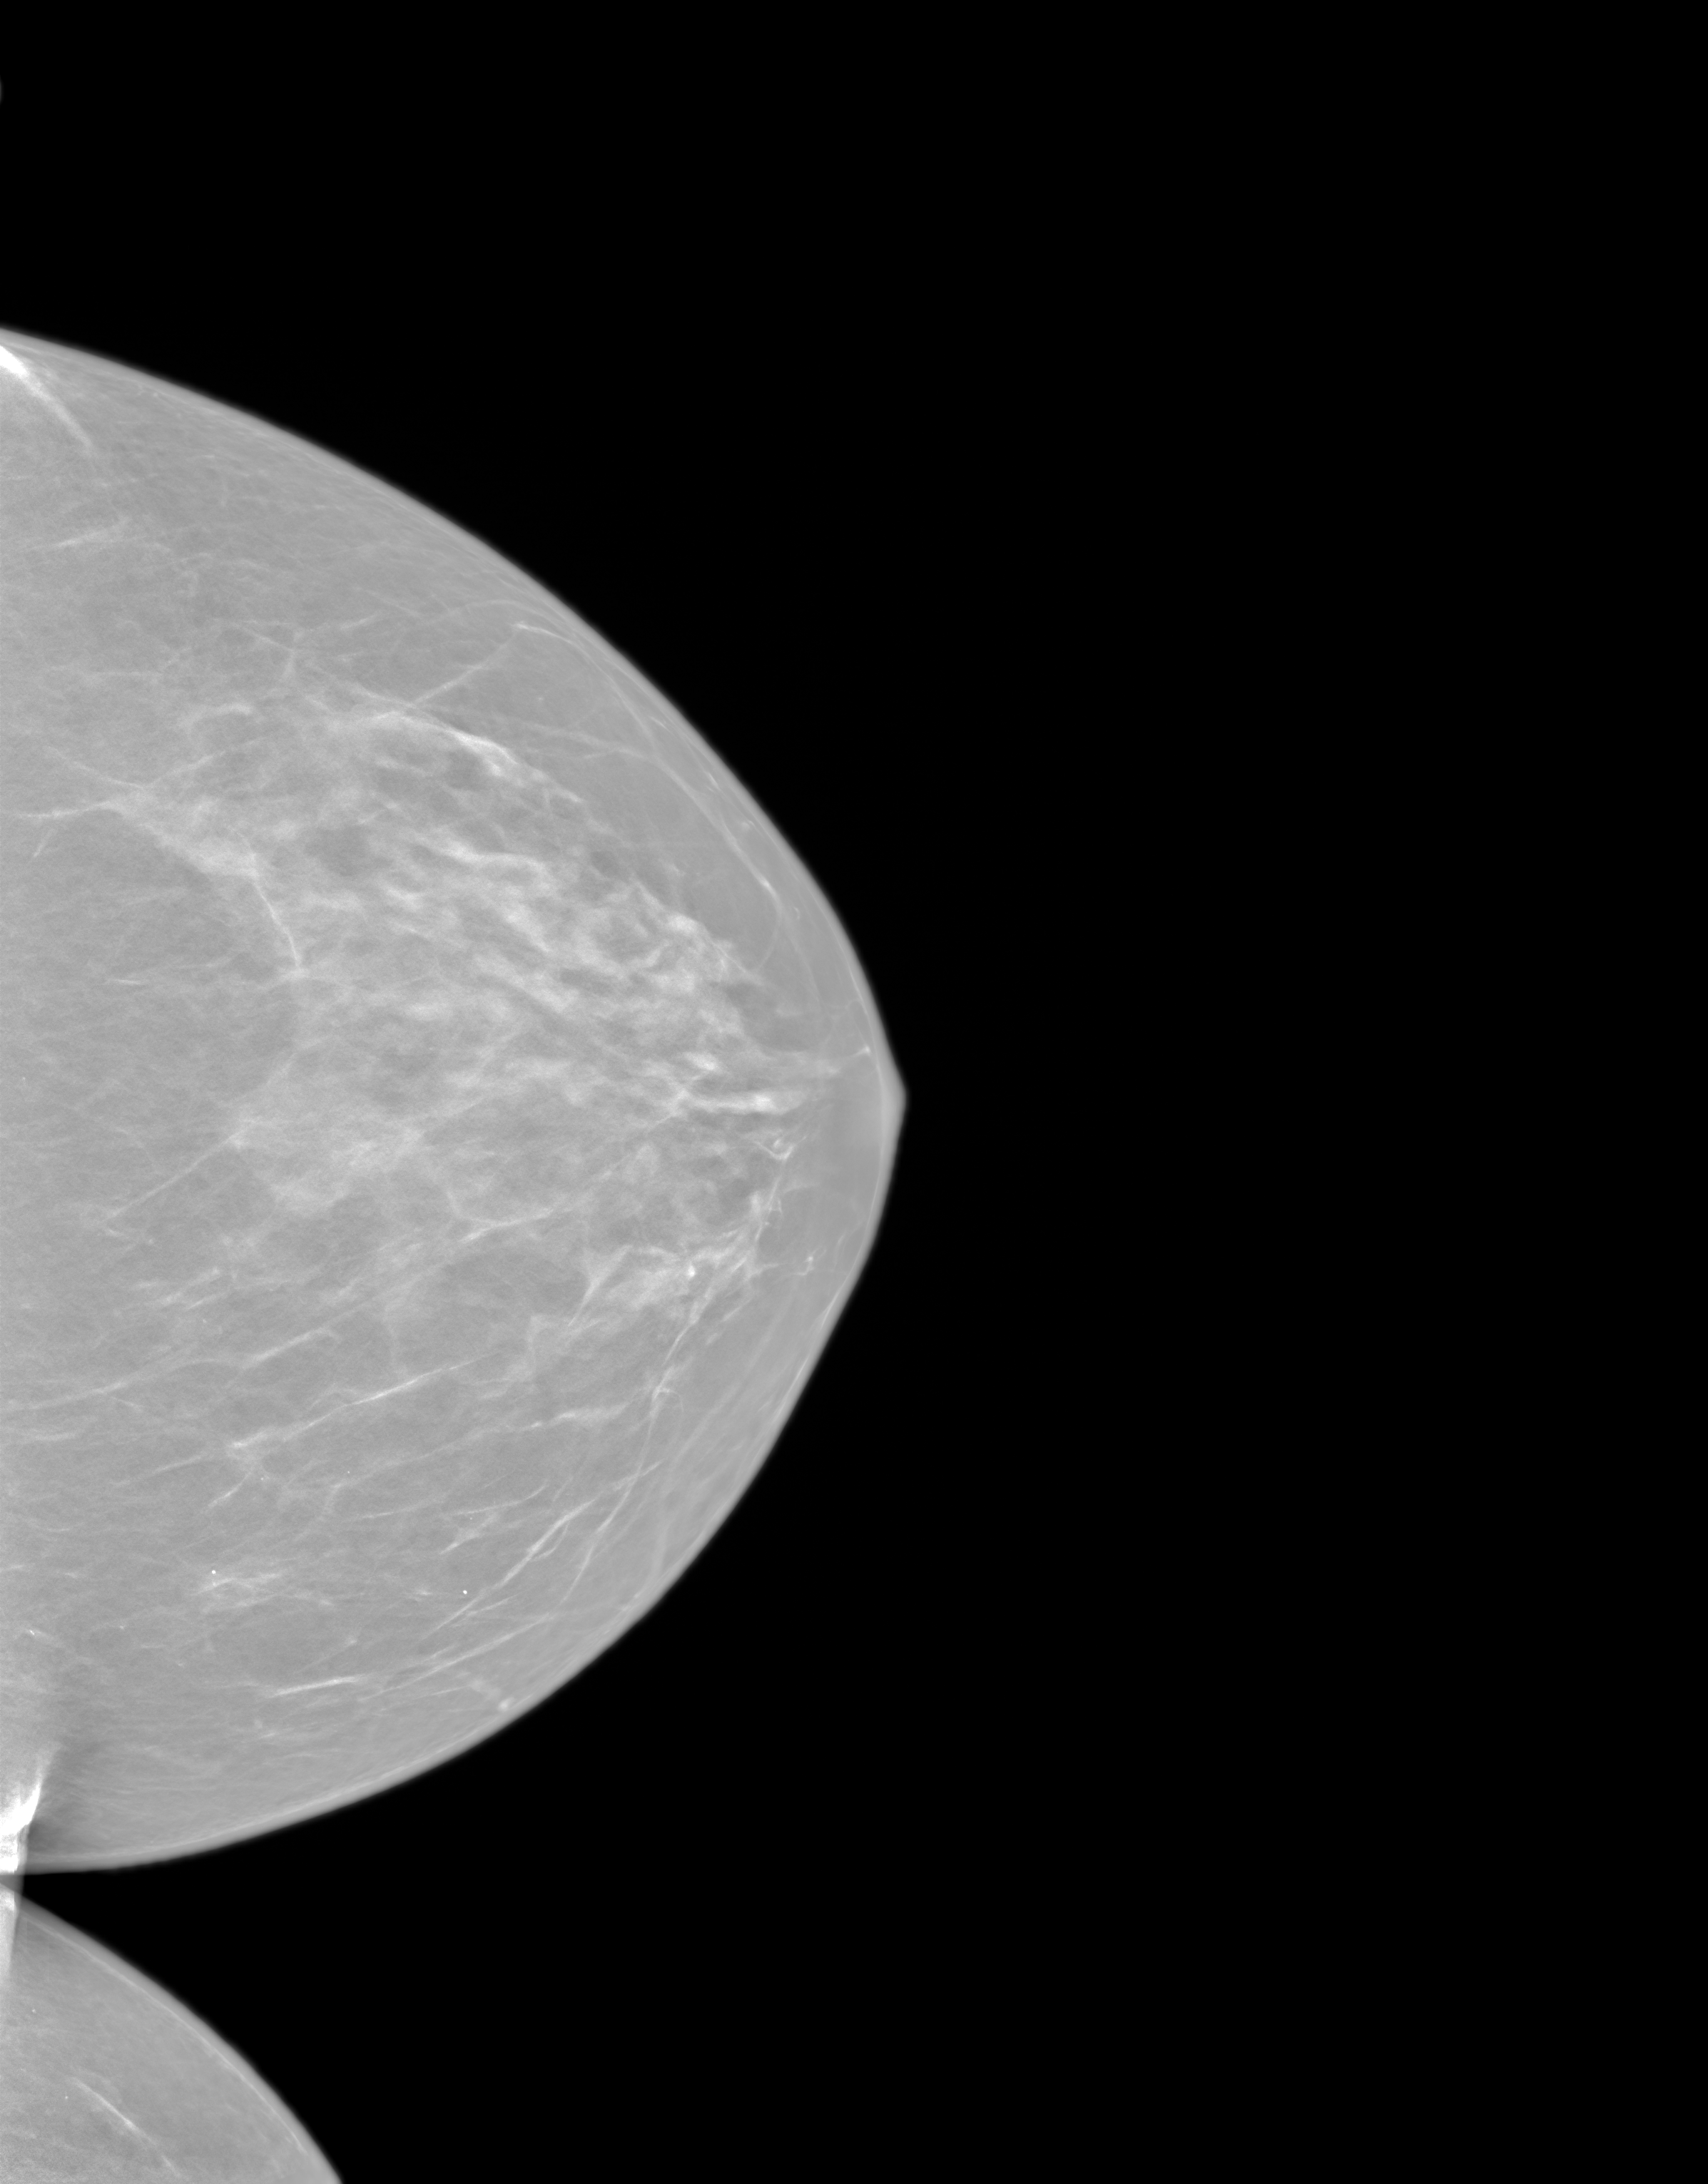
Synthetic 2-D view generated from a tomosynthesis acquisition (not an FFDM exposure), left breast, craniocaudal (CC) view, annual screening mammography examination, system: SenoIris_1SP1.1(421). Female patient, age 57 years.
Breast density at the screening exam (both breasts): scattered fibroglandular densities (BI-RADS density category b). Final BI-RADS category for the screening round (tomosynthesis exam, both breasts): category 1. Recall: no recall after this screen.